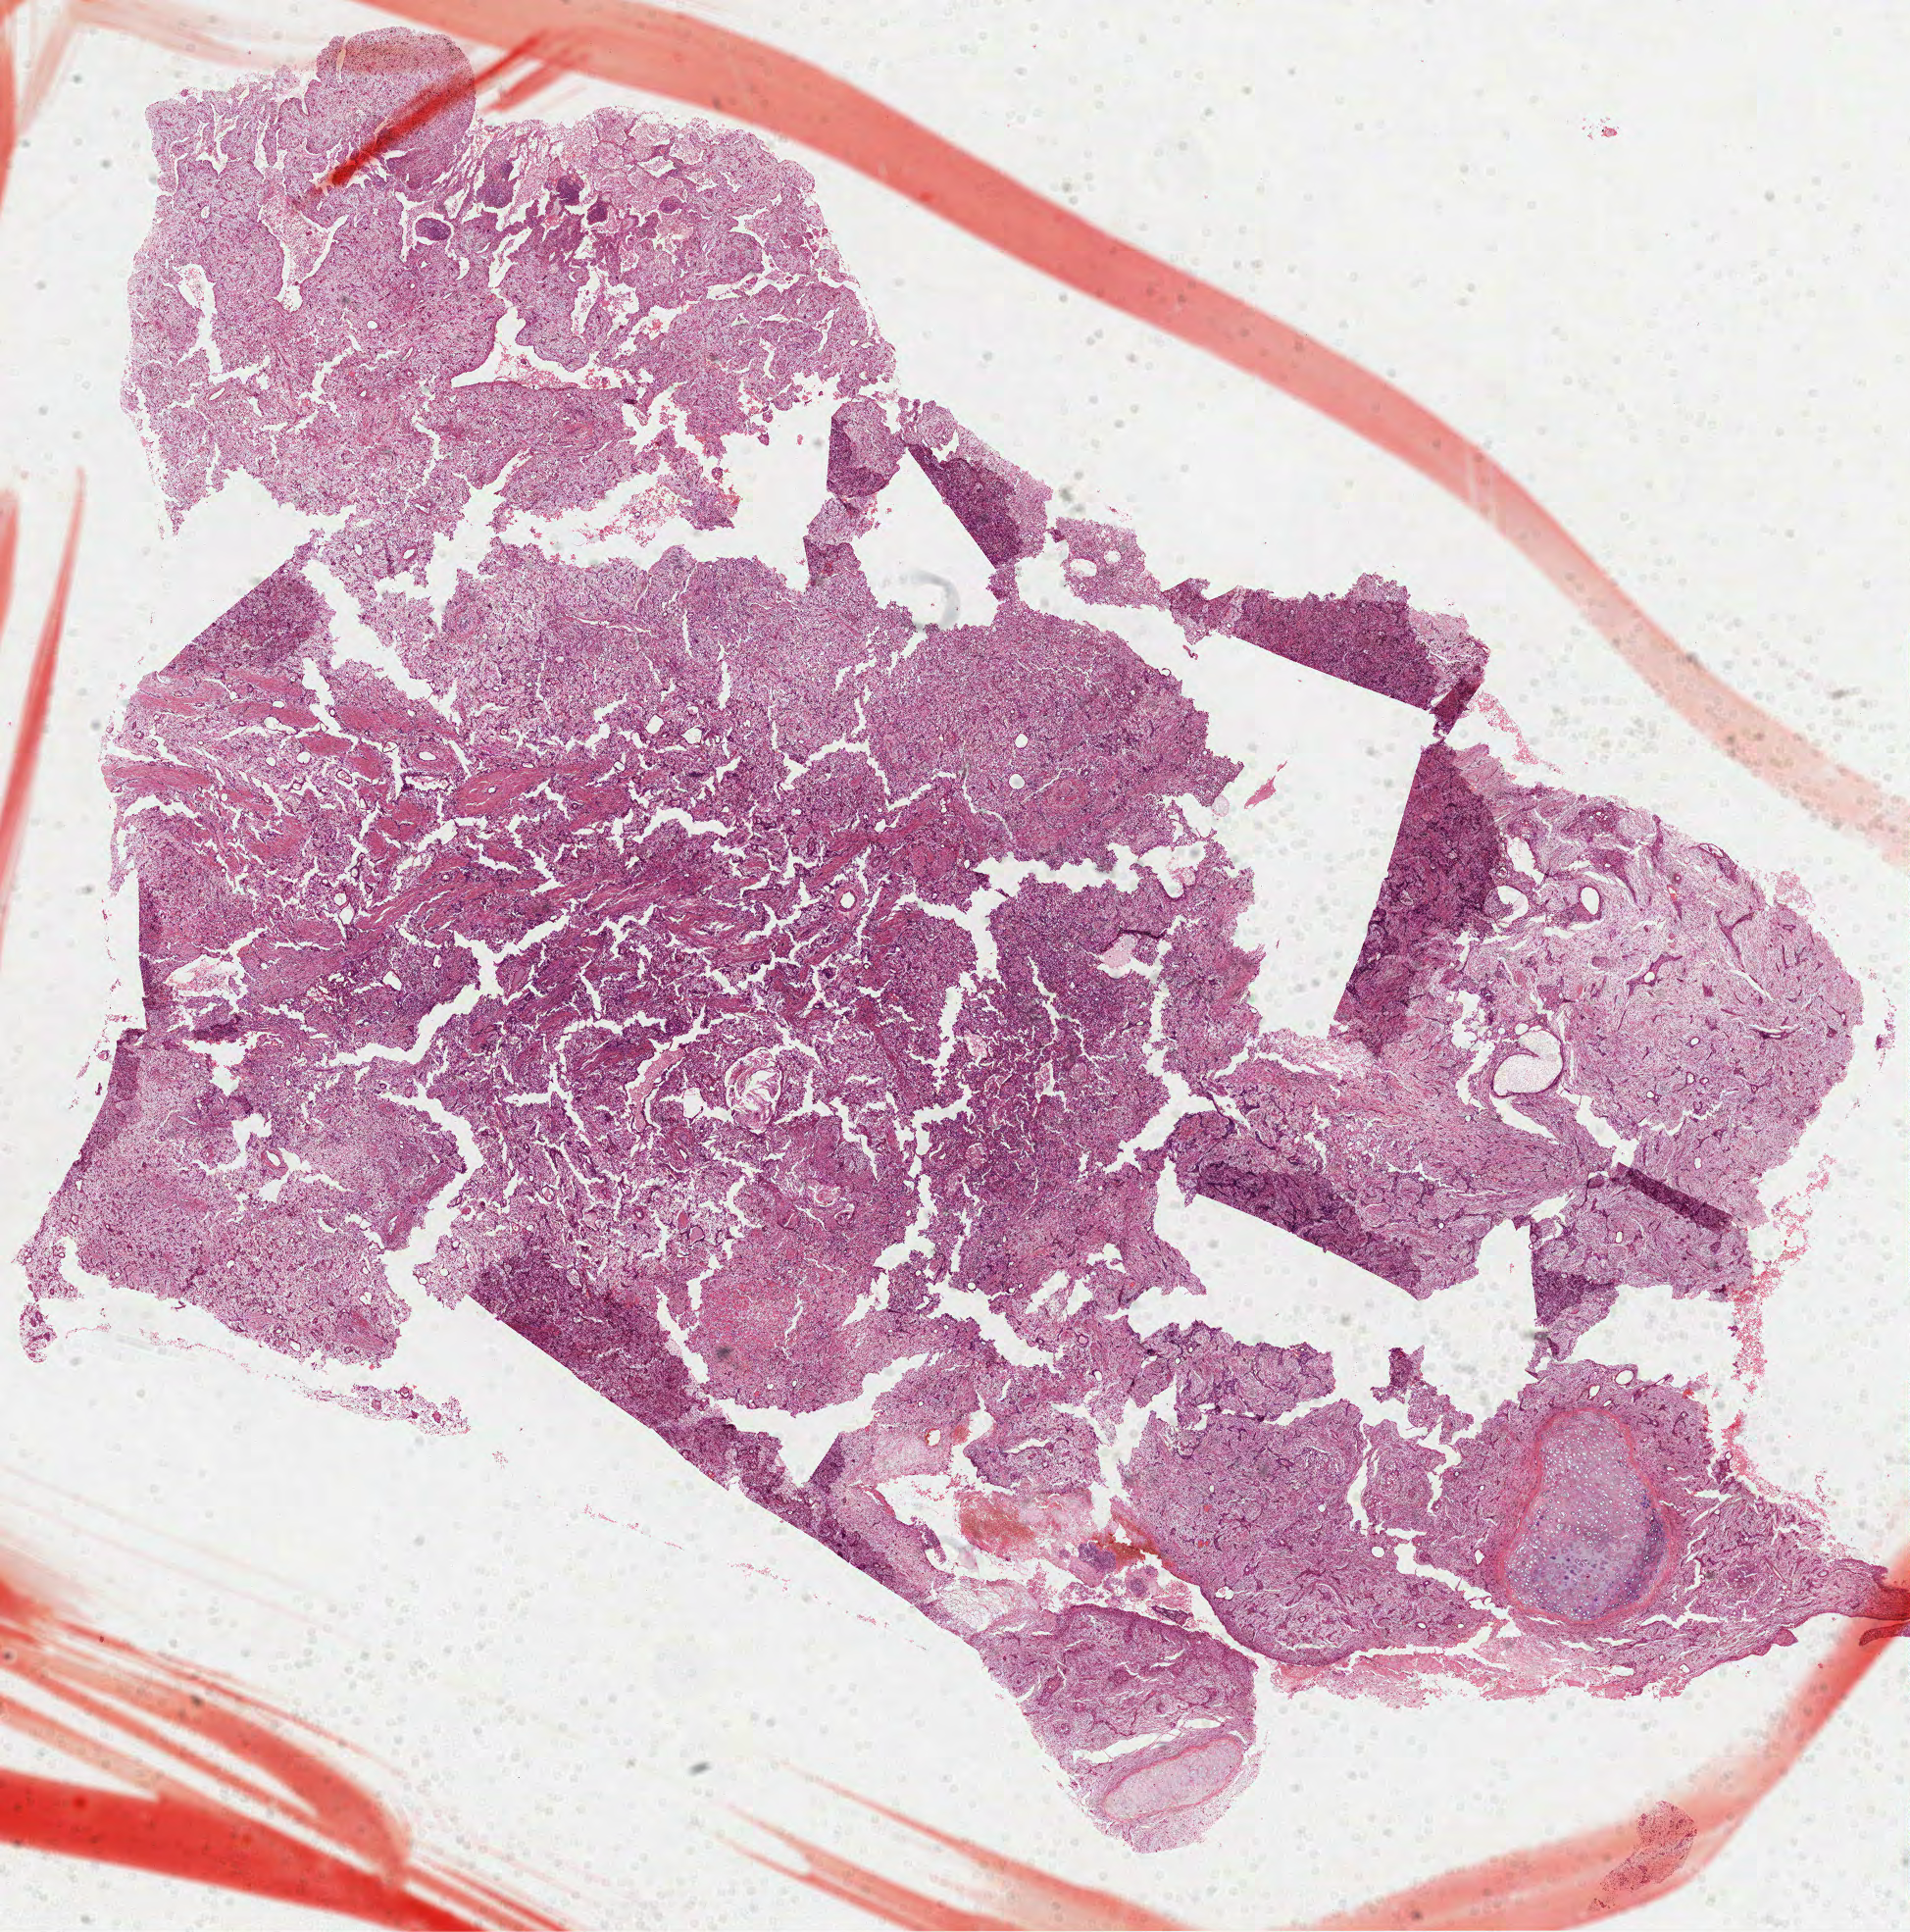
H&E whole-slide image — shown as a low-resolution overview of the whole scanned area (about 15.7 x 15.9 mm, from a 40x scan), formalin-fixed paraffin-embedded (FFPE) diagnostic section, sample: primary tumour, lung. Female, age 63 years at initial diagnosis.
TNM: T3 N0 M0. Diagnosis: Squamous cell carcinoma, NOS (upper lobe, lung). Laterality: left. AJCC pathologic stage: IIB (7th edition).